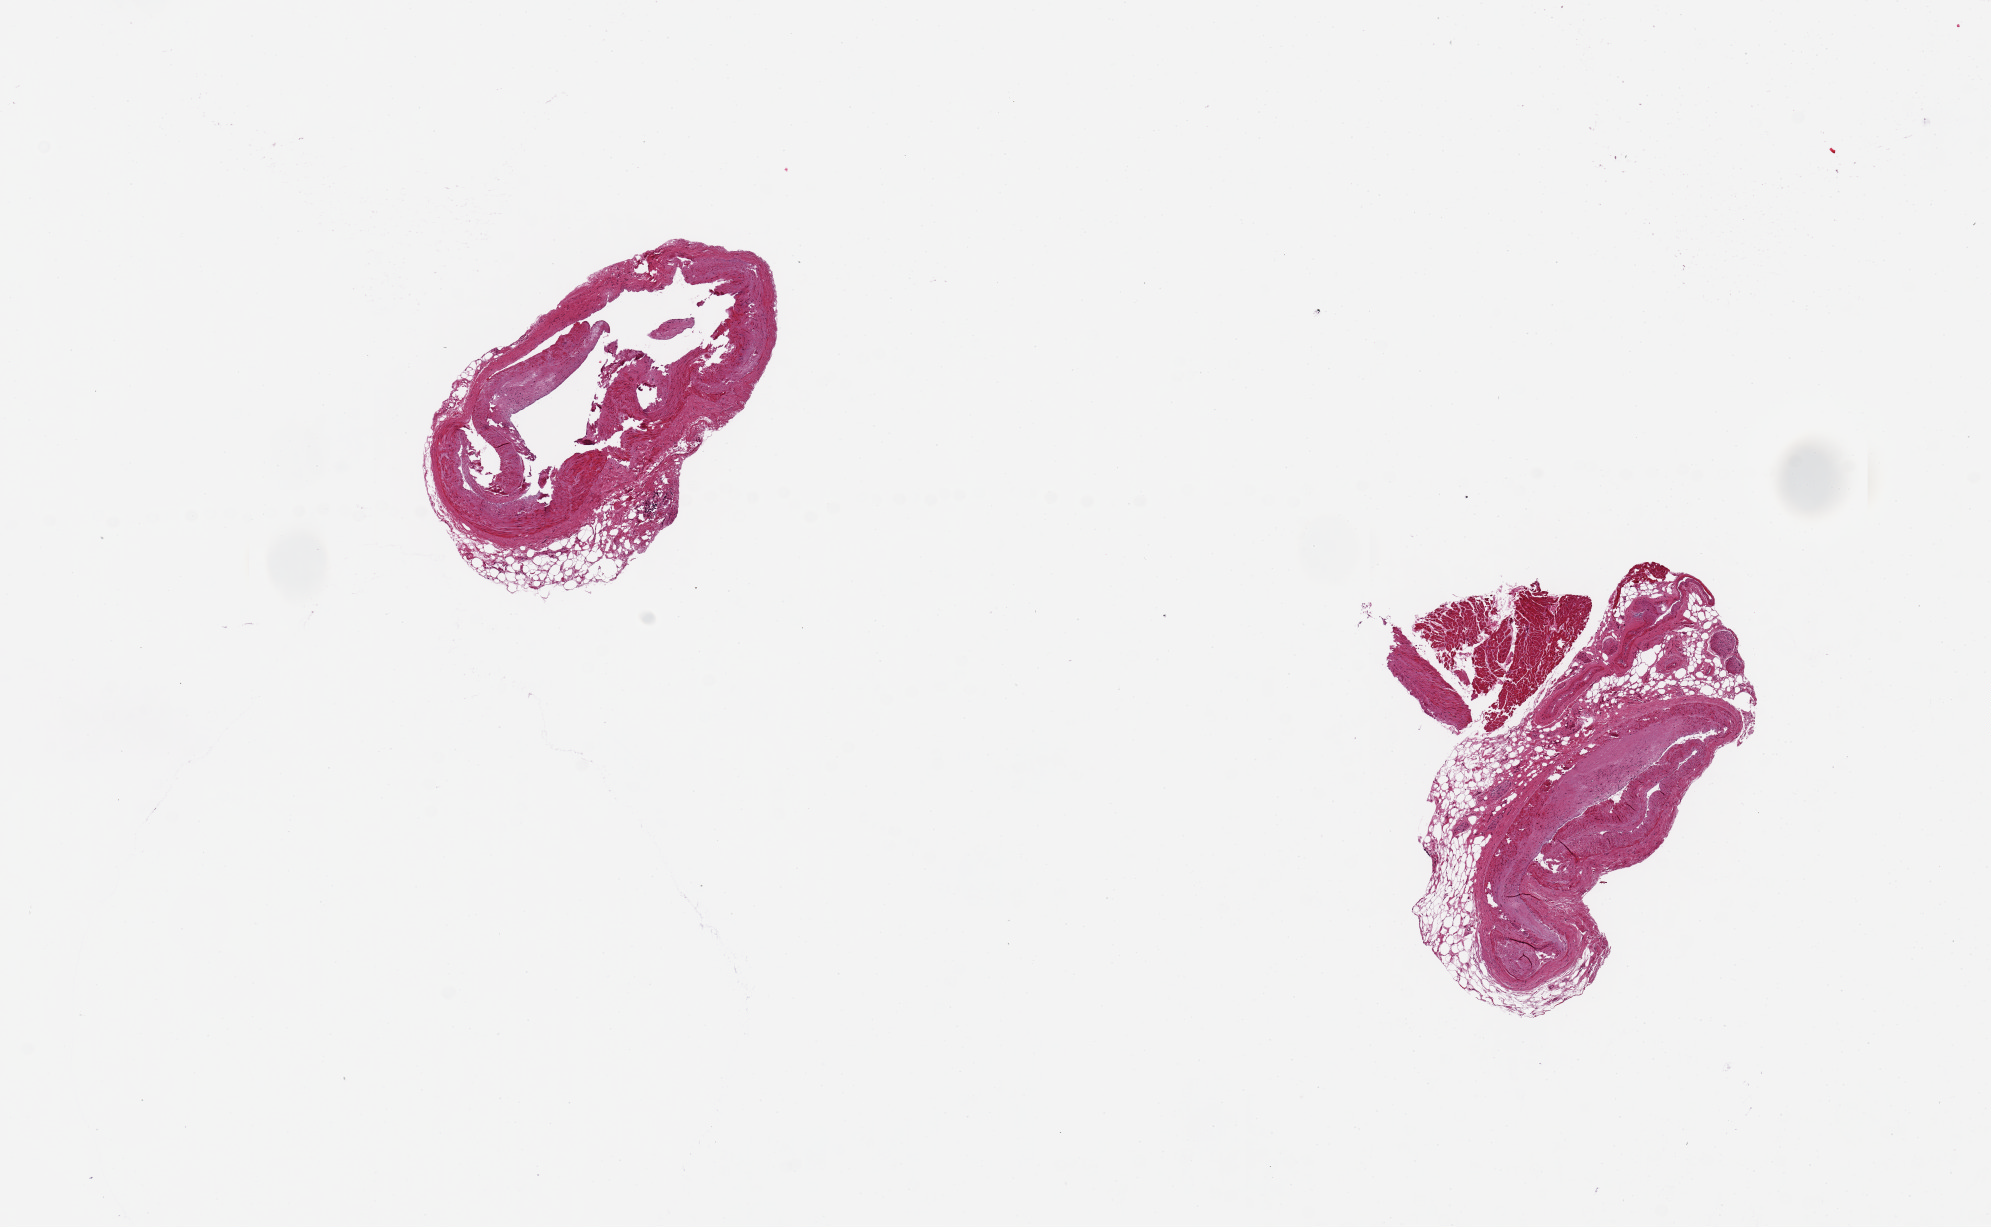
Digitized hematoxylin and eosin (H&E)-stained section, whole scanned area (about 15.8 x 9.7 mm, acquisition: 20x scan) shown as a low-resolution overview. PAXgene-fixed paraffin-embedded (PFPE) section. Sampled site (target tissue): coronary artery. Donor tissue sample. Male donor.
Review note (as recorded): 2 pieces ~2mm d. Subtotally occlusive atherosclerotic debris.